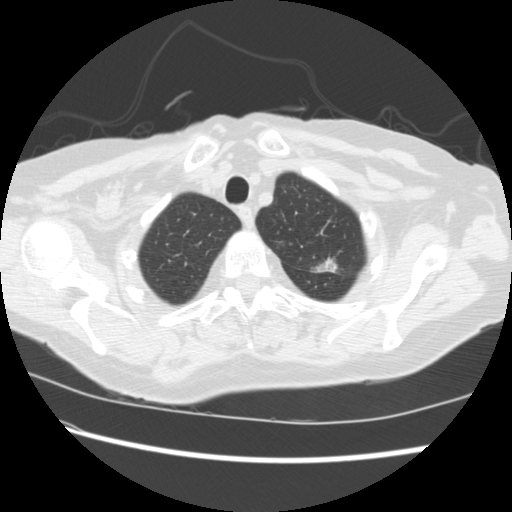
Low-dose screening chest CT, axial slice; baseline screening round; lung window (W 1500 / L -600 HU); standard (soft-tissue) reconstruction kernel (STANDARD); slice 35 of 224 in the series; 512 × 512 image matrix, field of view 340 × 340 mm. Female participant, aged 74 years at enrolment. Former smoker at enrolment.
Expert reader's lesion annotation, box from (x=298, y=248) to (x=348, y=285) px. The screening reader recorded 2 non-calcified nodules or masses ≥4 mm on this exam (left upper lobe, right lower lobe); which of them this box marks is not recorded. Later outcome: lung cancer diagnosed 309 days after this screen — non-small cell carcinoma, left upper lobe, stage IV (AJCC 6th edition).